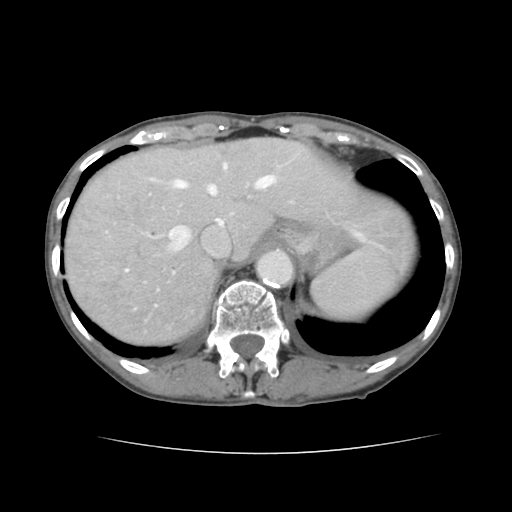
Contrast-enhanced abdominal CT, one axial slice. Slice 113 of 136 in the series (ordered by position). Intravenous contrast given. Soft-tissue window (W 400 / L 40 HU). 2.5 mm slice thickness. 512 × 512 image matrix, field of view 319 × 319 mm. Female patient, age 77 years. Case-level facts recorded for this patient, not image findings: diagnosis: colorectal cancer liver metastases, imaged before liver resection; multiple liver metastases: yes; largest metastasis: 3 cm; chemotherapy before resection: yes.
Structures marked on this image (manually delineated by an expert):
- hepatic veins: box from (x=132, y=164) to (x=274, y=256) px
- liver: (x=65, y=138)–(x=412, y=344)
- planned liver remnant (the part of the liver to remain after resection): (x=169, y=138)–(x=410, y=263)